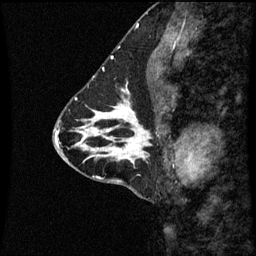
Breast MRI (dynamic contrast-enhanced), one sagittal slice. Slice 27 of 60 in the series (ordered by position). Dynamic contrast-enhanced series, image 2 of 3 at this slice position (ordered by acquisition). 1.5 T. TE 4.2 ms, TR 8.9 ms. 2 mm slice thickness. 256 × 256 image matrix. Female patient, age 43 years. From the clinical record (not read from this slice): setting: breast cancer imaged before/during neoadjuvant chemotherapy; receptor status: HR-positive, HER2-negative.
Outlined on this slice (semi-automatically segmented with operator editing):
- analysis volume of interest (the breast-tissue region the enhancement analysis was run in; not a lesion): box from (x=110, y=100) to (x=170, y=163) px
- tumour enhancement mask (voxels above the 70 % enhancement threshold inside the analysis volume of interest): (x=117, y=102)–(x=142, y=163)